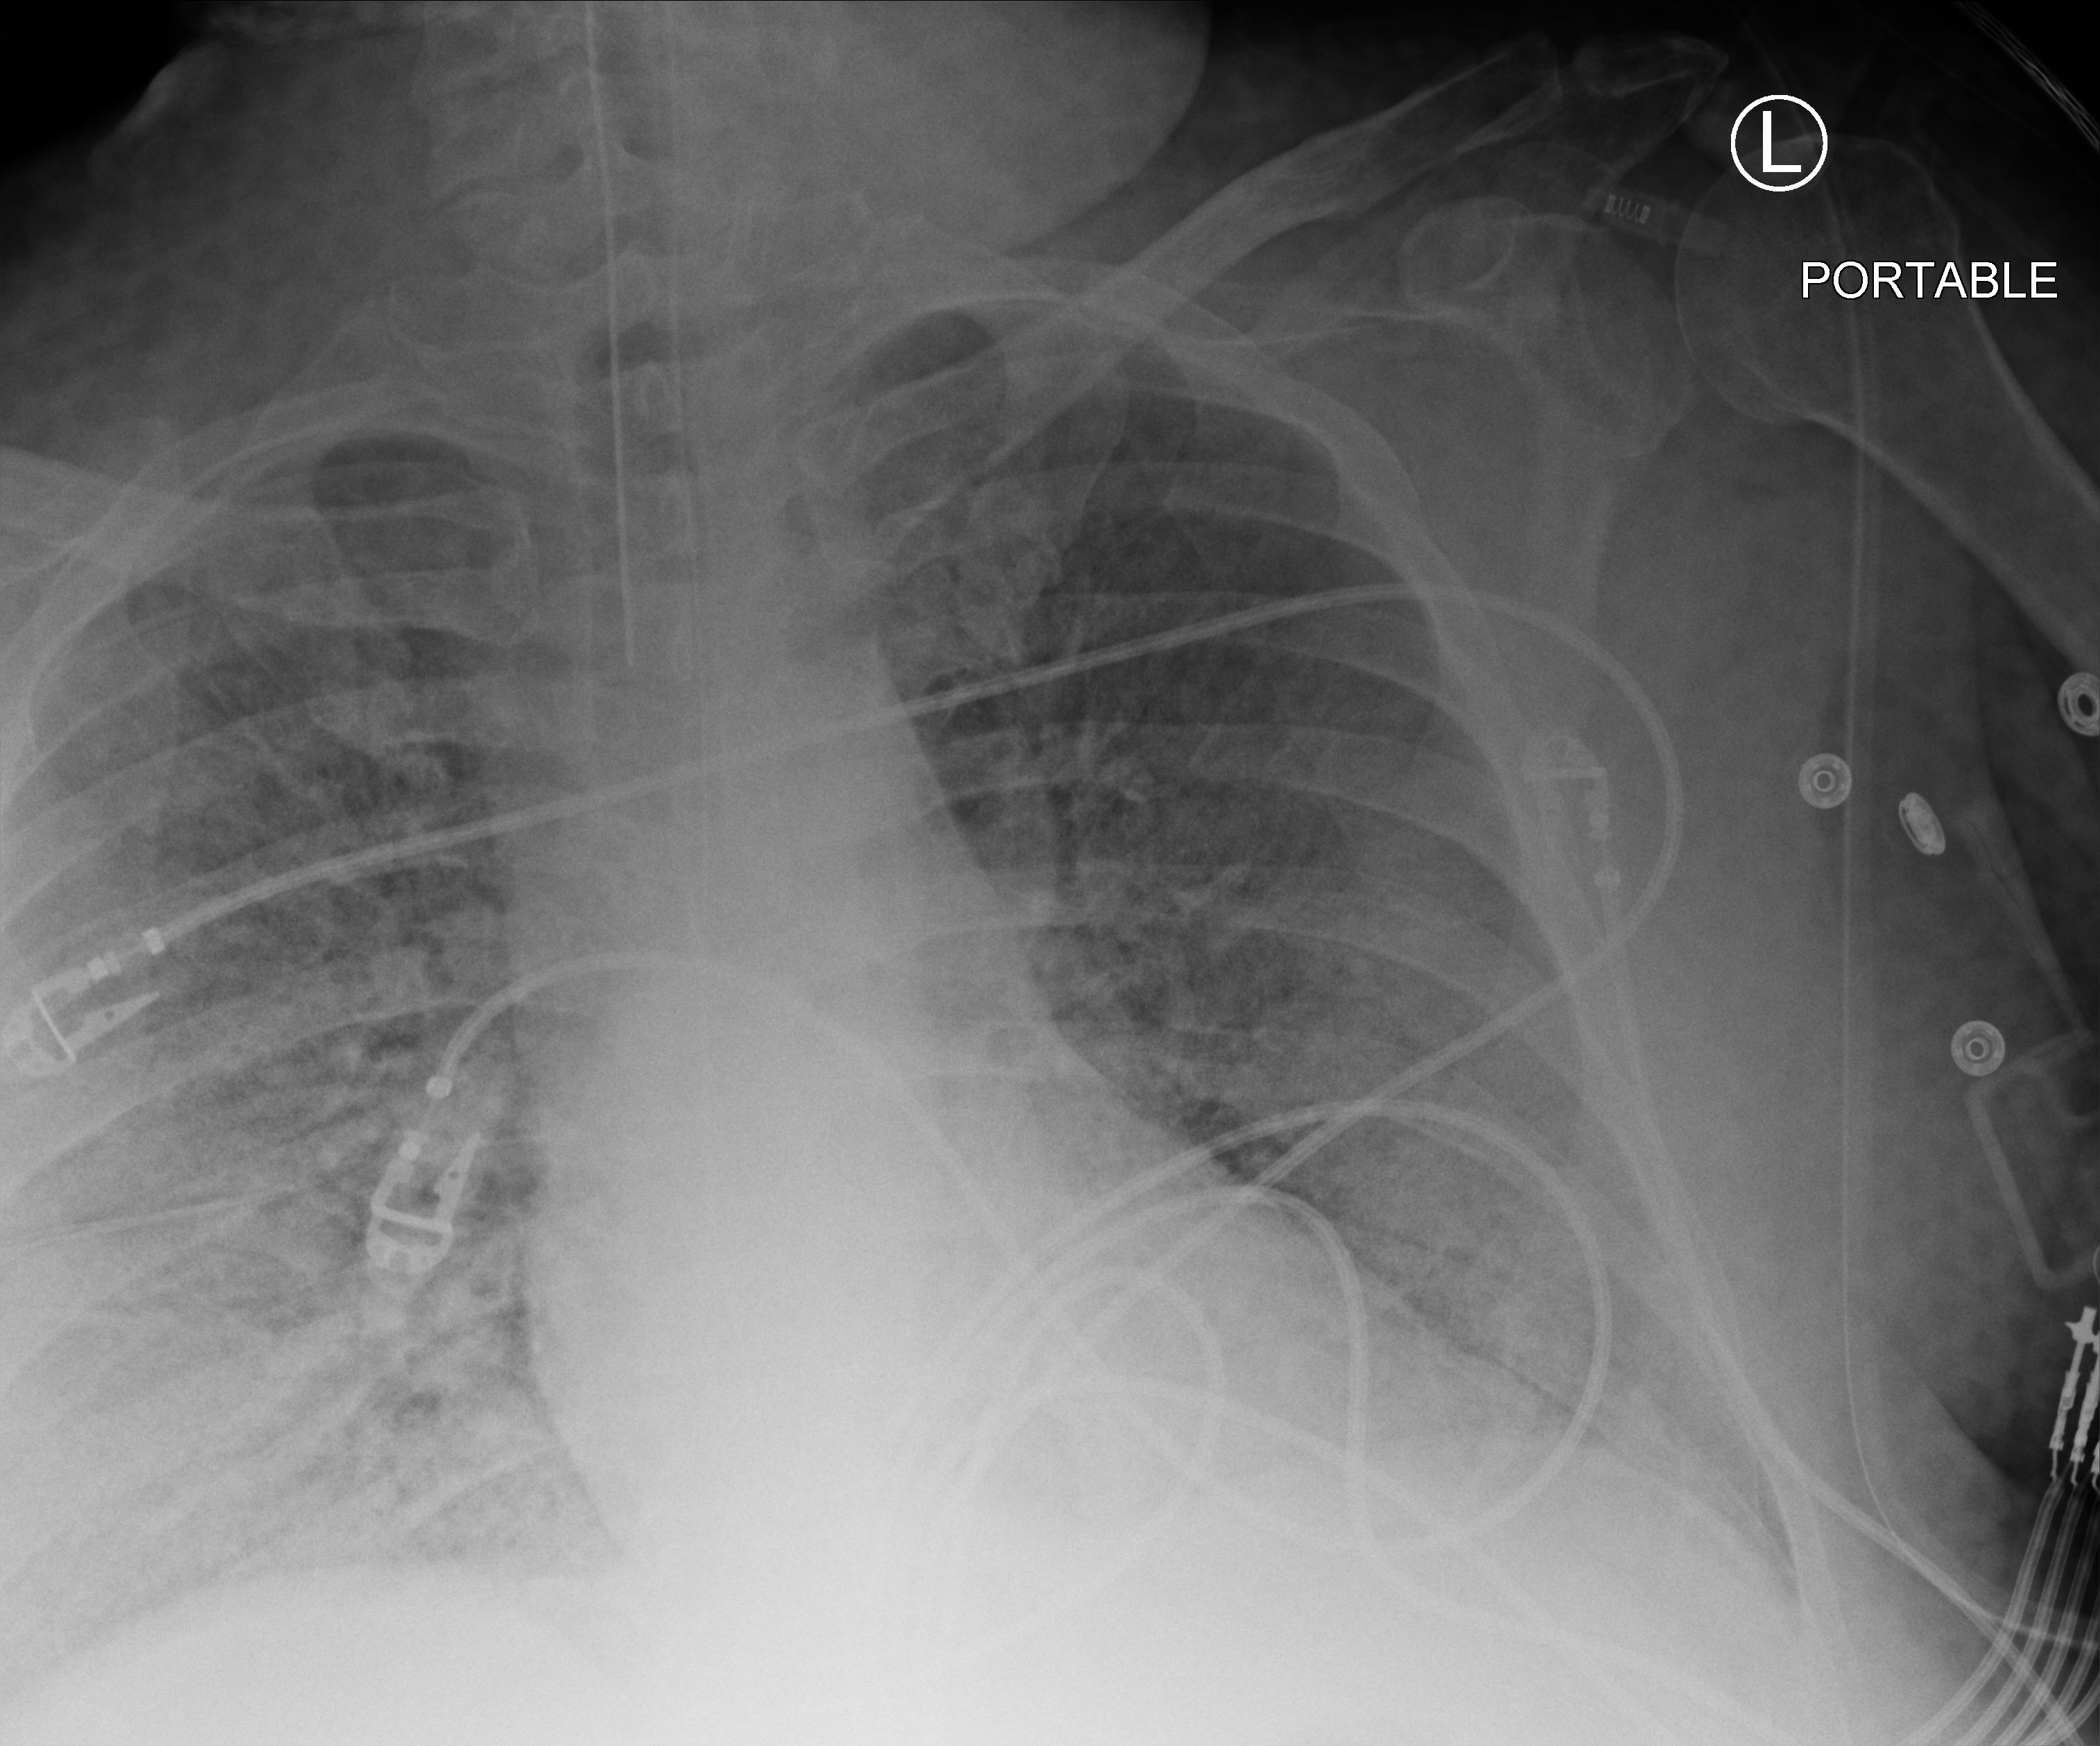
Bedside chest radiograph (computed radiography), anteroposterior (AP) projection. Patient hospitalised with COVID-19, aged 18–59 years.
Hospital-stay facts (about this admission, not read from this image; timing relative to this image not recorded): admitted to intensive care during this hospital stay: yes; chronic kidney disease (admission record): no; smoking status (admission record): never.